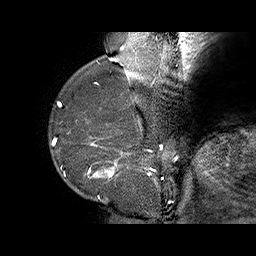
Breast MRI (dynamic contrast-enhanced), one sagittal slice. Position 13 of 70 along the scan axis. Dynamic contrast-enhanced series, time point 2 of 6 at this slice position (early post-contrast). 1.5 T. TE 4.5 ms, TR 32.4 ms. 3 mm slice thickness. 256 × 256 image matrix. Female patient. From the clinical record (not read from this slice): setting: breast cancer imaged before/during neoadjuvant chemotherapy; receptor status: HR-positive, HER2-negative.
Structures marked on this image (semi-automatic segmentation, software-assisted and operator-edited):
- analysis volume of interest (the breast-tissue region the enhancement analysis was run in; not a lesion): bounding box [x1, y1, x2, y2] px = [71, 128, 159, 202]
- tumour enhancement mask (voxels above the 100 % enhancement threshold inside the analysis volume of interest): [87, 136, 157, 199]